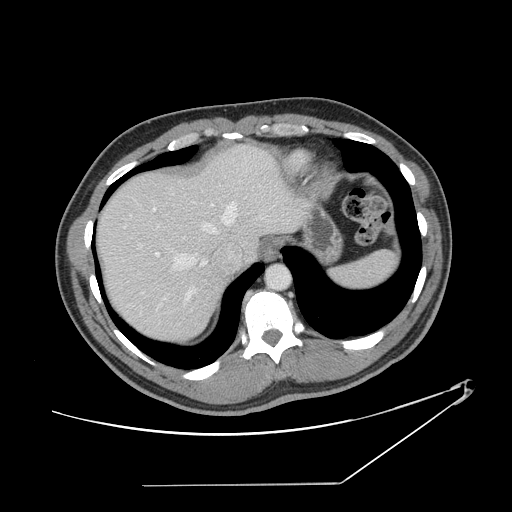
Contrast-enhanced abdominal CT, one axial slice; position 121 of 152 along the scan axis; reconstruction kernel STANDARD; 120 kVp; soft-tissue window (W 400 / L 40 HU); 512 × 512 image matrix, field of view 432 × 432 mm. Male patient, age 45 years. Case-level facts recorded for this patient, not image findings: diagnosis: colorectal cancer liver metastases, imaged before liver resection; multiple liver metastases: no; largest metastasis: 1 cm; disease in both lobes: no.
Annotated regions visible in this slice (expert manual segmentation):
- hepatic veins: bounding box (x1, y1, x2, y2) in pixels: (123, 201, 238, 303)
- liver: (99, 148, 301, 341)
- planned liver remnant (the part of the liver to remain after resection): (100, 173, 234, 341)
- portal vein (with intrahepatic branches): (155, 252, 192, 311)